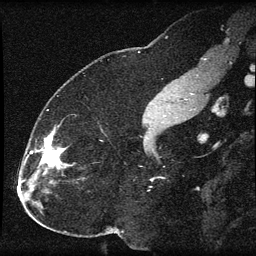
Breast MRI (dynamic contrast-enhanced), one sagittal slice; slice 29 of 60 in the series (ordered by position); dynamic contrast-enhanced series, image 2 of 3 at this slice position (ordered by acquisition); 1.5 T; TE 4.2 ms, TR 8.2 ms; 2 mm slice thickness; 256 × 256 image matrix, field of view 180 × 180 mm. Patient: female, 32 years.
Outlined on this slice (semi-automatic segmentation, software-assisted and operator-edited):
- analysis volume of interest (the breast-tissue region the enhancement analysis was run in; not a lesion): bounding box <31,129,75,184> (left, top, right, bottom; pixels)
- tumour enhancement mask (voxels above the 70 % enhancement threshold inside the analysis volume of interest): <31,136,65,173>